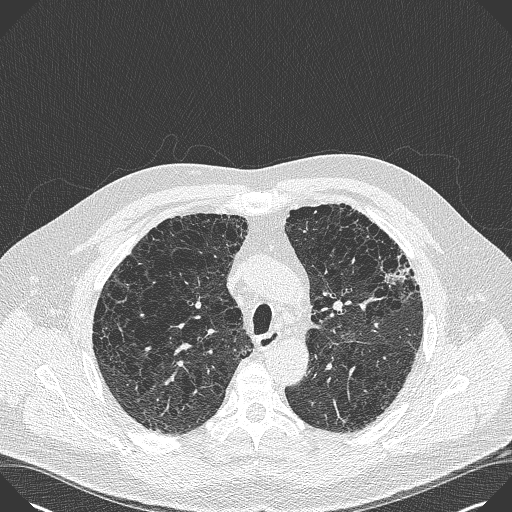
Low-dose screening chest CT, axial slice, baseline screening round, lung window (W 1500 / L -600 HU), slice 119 of 383 in the series, 512 × 512 image matrix, field of view 380 × 380 mm. Male participant, aged 59 years at enrolment. Current smoker at enrolment.
Lesion marked by an expert reader, box from (x=374, y=242) to (x=427, y=293) px. Screening reader's record for this exam: no non-calcified nodule ≥4 mm recorded. Participant outcome: lung cancer diagnosed 909 days after this screen — bronchiolo-alveolar carcinoma, mixed mucinous and non-mucinous, left upper lobe, stage IA (AJCC 6th edition), 20 mm at pathology.